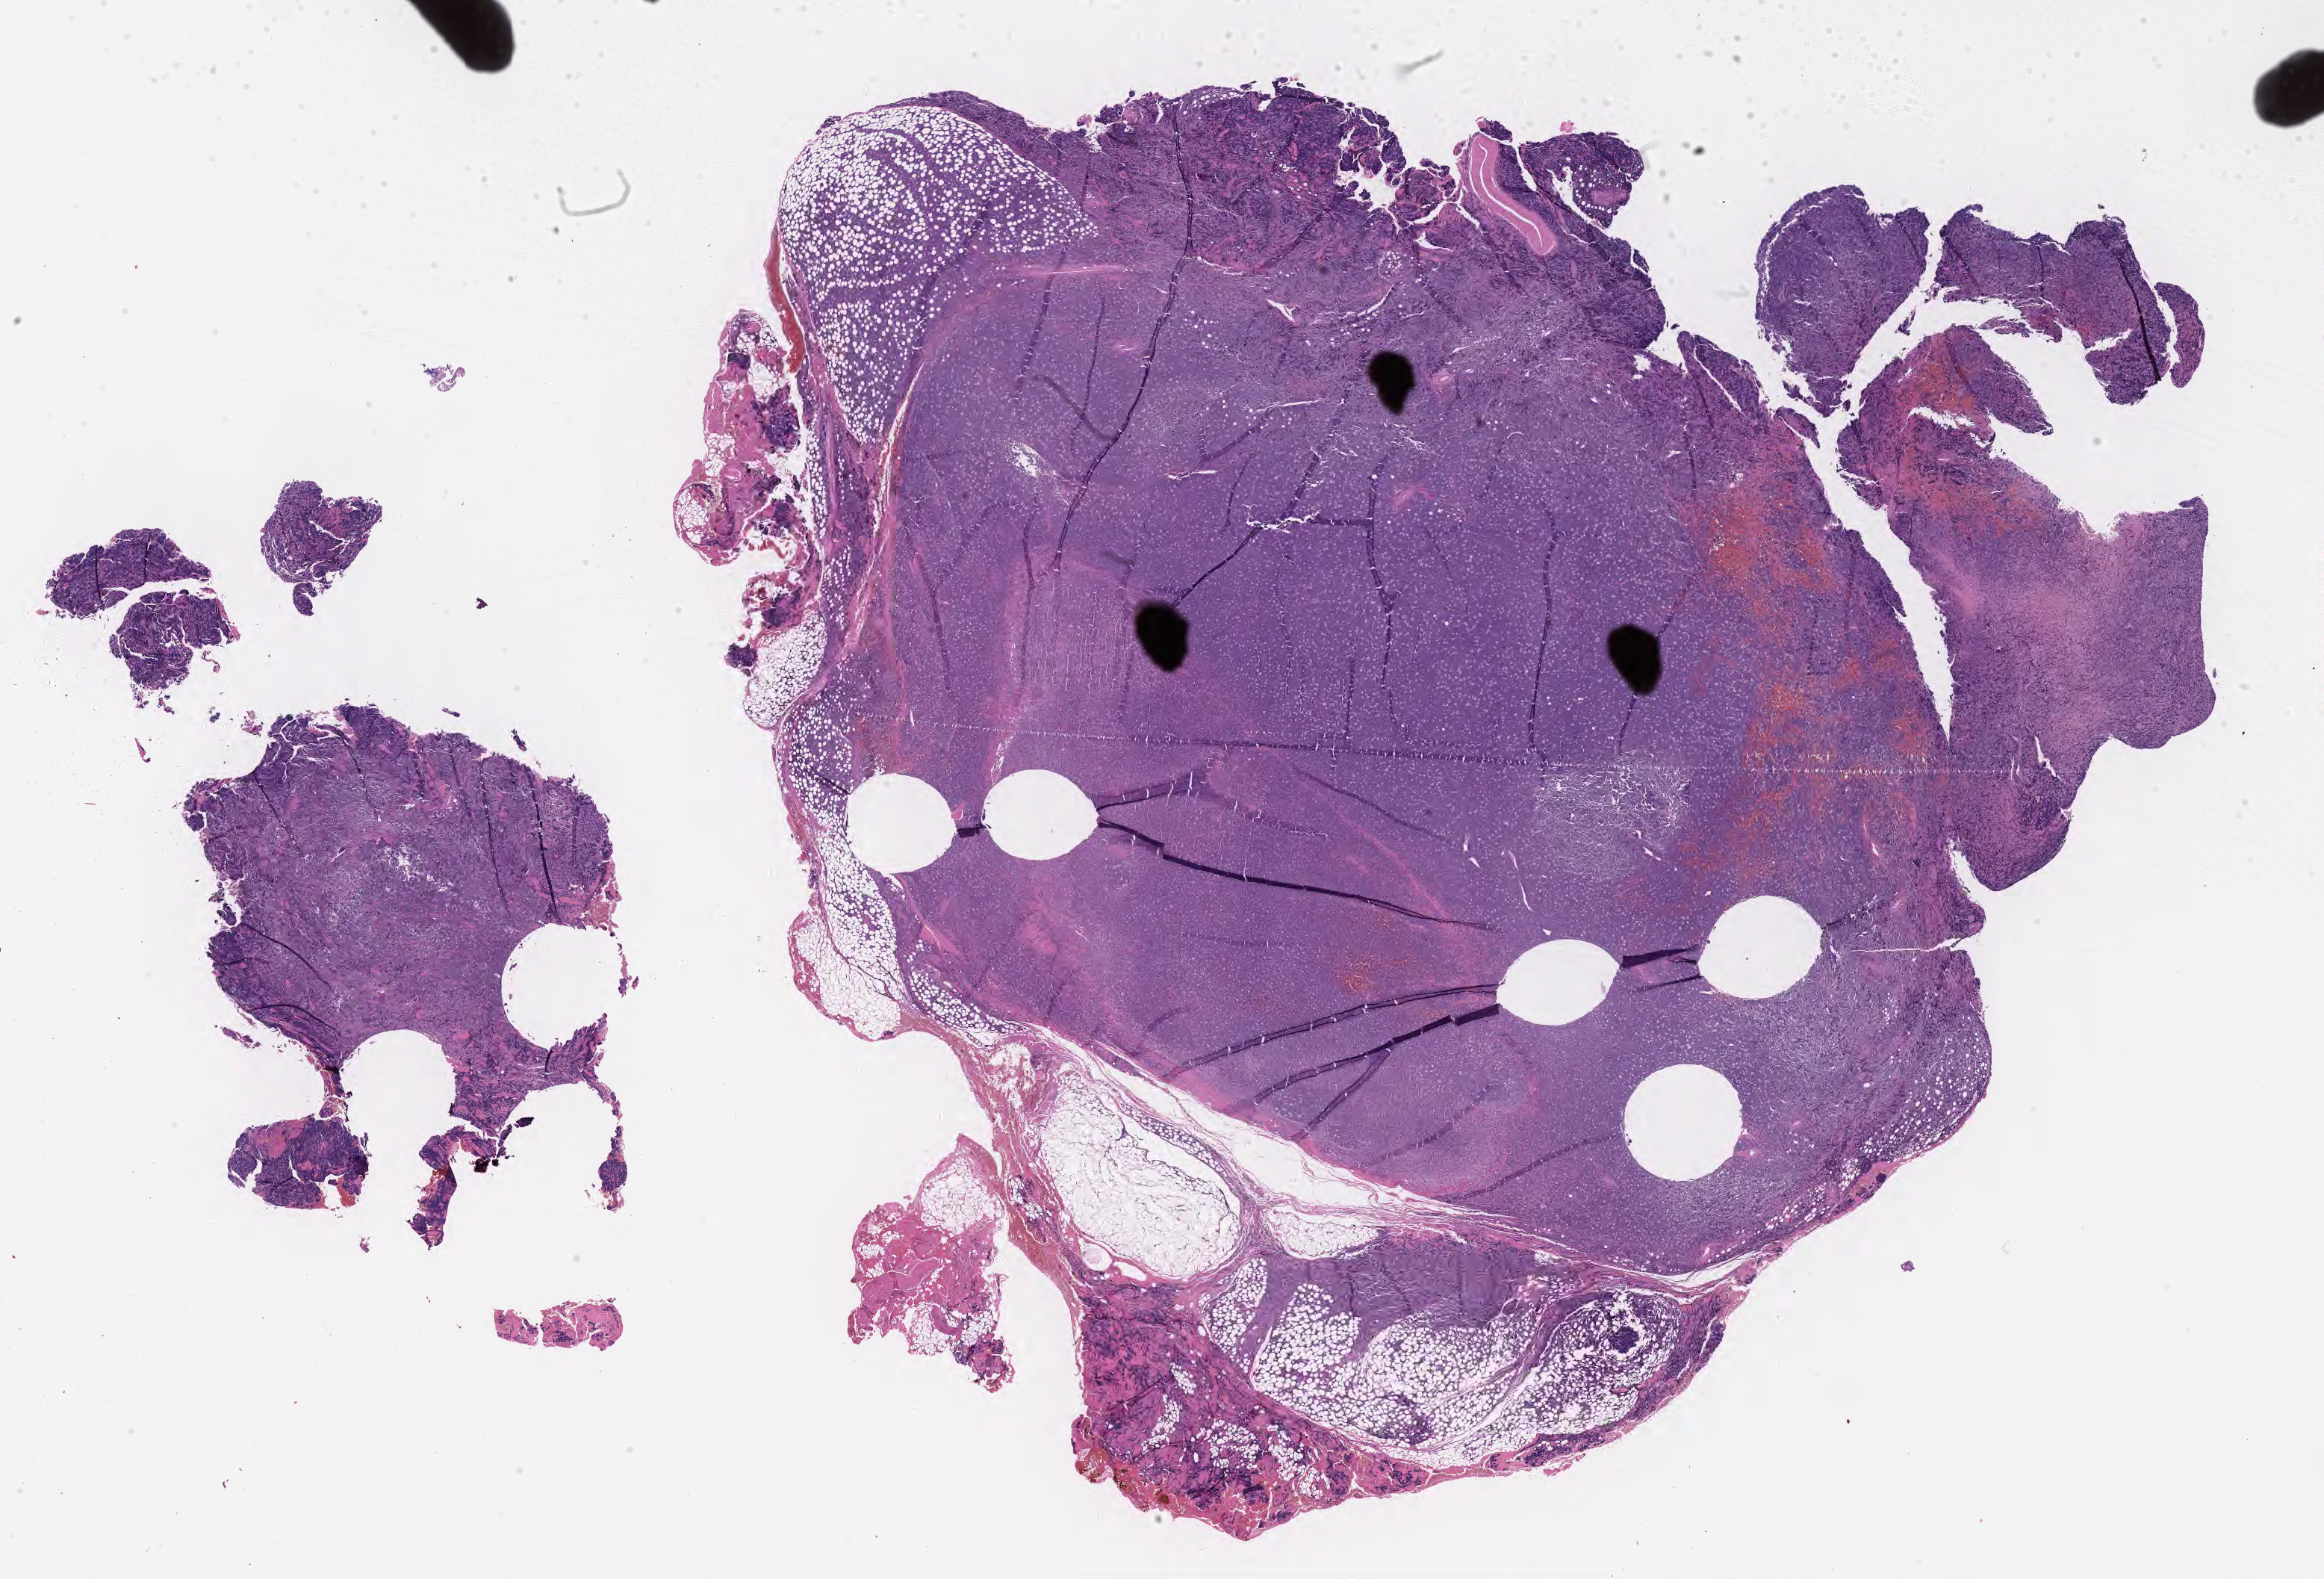
Hematoxylin and eosin (H&E) whole-slide image, shown as a low-resolution overview of the whole scanned area (about 25.2 x 17.1 mm). Patient: male, 40 years old.
- specimen: tumor tissue